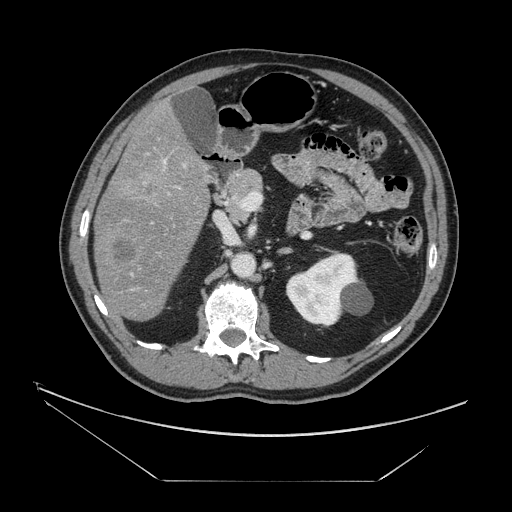
Contrast-enhanced abdominal CT, one axial slice. Position 74 of 161 along the scan axis. Reconstruction kernel STANDARD. Intravenous contrast given. Soft-tissue window (W 400 / L 40 HU). 2.5 mm slice thickness. 512 × 512 image matrix, field of view 440 × 440 mm. Male patient, age 65 years. From the clinical record (not read from this slice): diagnosis: colorectal cancer liver metastases, imaged before liver resection; multiple liver metastases: yes; largest metastasis: 4.2 cm; disease in both lobes: yes.
Structures marked on this image (manually delineated by an expert):
- liver: box from (x=95, y=107) to (x=209, y=321) px
- portal vein (with intrahepatic branches): (x=164, y=160)–(x=185, y=188)
- liver metastasis: (x=115, y=240)–(x=136, y=262)
- liver metastasis: (x=144, y=183)–(x=154, y=198)